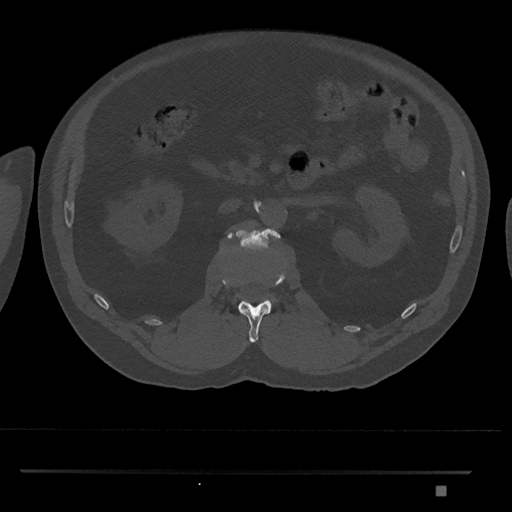
CT including the spine, one axial slice. Slice 797 of 1134 in the series (ordered by position). Reconstruction kernel Br40s/3. Bone window (W 1800 / L 400 HU). 0.5 mm slice thickness. 512 × 512 image matrix, field of view 429 × 429 mm. Male patient, age 65 years. Case-level facts recorded for this patient, not image findings: primary cancer: prostate.
Annotated regions visible in this slice (semi-automatic segmentation, software-assisted and operator-edited):
- L1 vertebra: bounding box (x1, y1, x2, y2) in pixels: (223, 265, 286, 343)
- L2 vertebra: (227, 228, 281, 302)